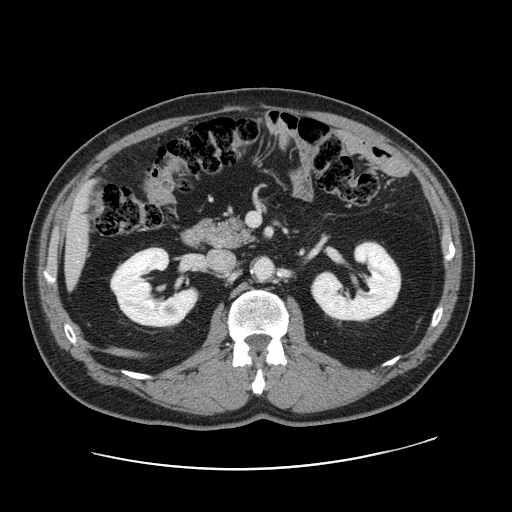
Contrast-enhanced abdominal CT, one axial slice; position 70 of 178 along the scan axis; soft-tissue window (W 400 / L 40 HU); 2.5 mm slice thickness; 512 × 512 image matrix, field of view 403 × 403 mm. Male patient, age 63 years. Case-level facts recorded for this patient, not image findings: diagnosis: colorectal cancer liver metastases, imaged before liver resection; multiple liver metastases: yes; largest metastasis: 8 cm.
Outlined on this slice (expert manual segmentation):
- liver: bounding box (x1, y1, x2, y2) in pixels: (66, 190, 91, 280)